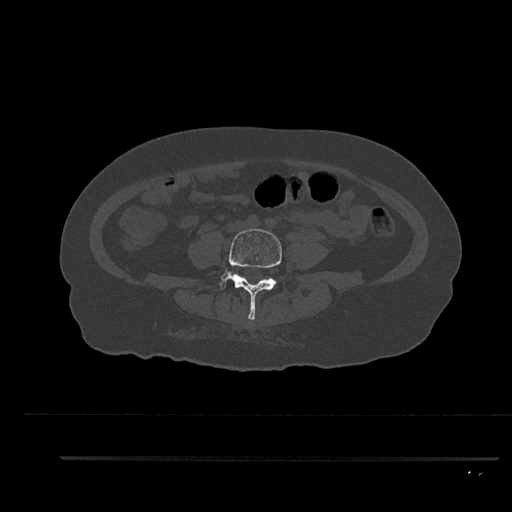
CT including the spine, one axial slice. Slice 15 of 797 in the series (ordered by position). Reconstruction kernel Br40s/3. 120 kVp. Bone window (W 1800 / L 400 HU). 512 × 512 image matrix. Female patient, age 44 years. Case-level facts recorded for this patient, not image findings: primary cancer: renal.
Structures marked on this image (semi-automatic segmentation, software-assisted and operator-edited):
- L4 vertebra: bounding box (x1, y1, x2, y2) in pixels: (217, 229, 282, 320)